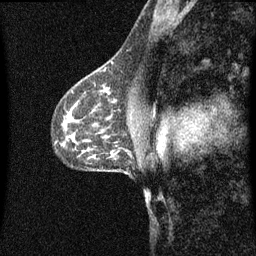
Breast MRI (dynamic contrast-enhanced), one sagittal slice; dynamic contrast-enhanced series, image 2 of 3 at this slice position (ordered by acquisition); 1.5 T; TE 4.2 ms, TR 8.4 ms; 2 mm slice thickness; 256 × 256 image matrix, field of view 200 × 200 mm. Patient: female, 41 years.
Annotated regions visible in this slice (semi-automatic segmentation, software-assisted and operator-edited):
- analysis volume of interest (the breast-tissue region the enhancement analysis was run in; not a lesion): bounding box <94,72,119,97> (left, top, right, bottom; pixels)
- tumour enhancement mask (voxels above the 70 % enhancement threshold inside the analysis volume of interest): <102,84,111,95>